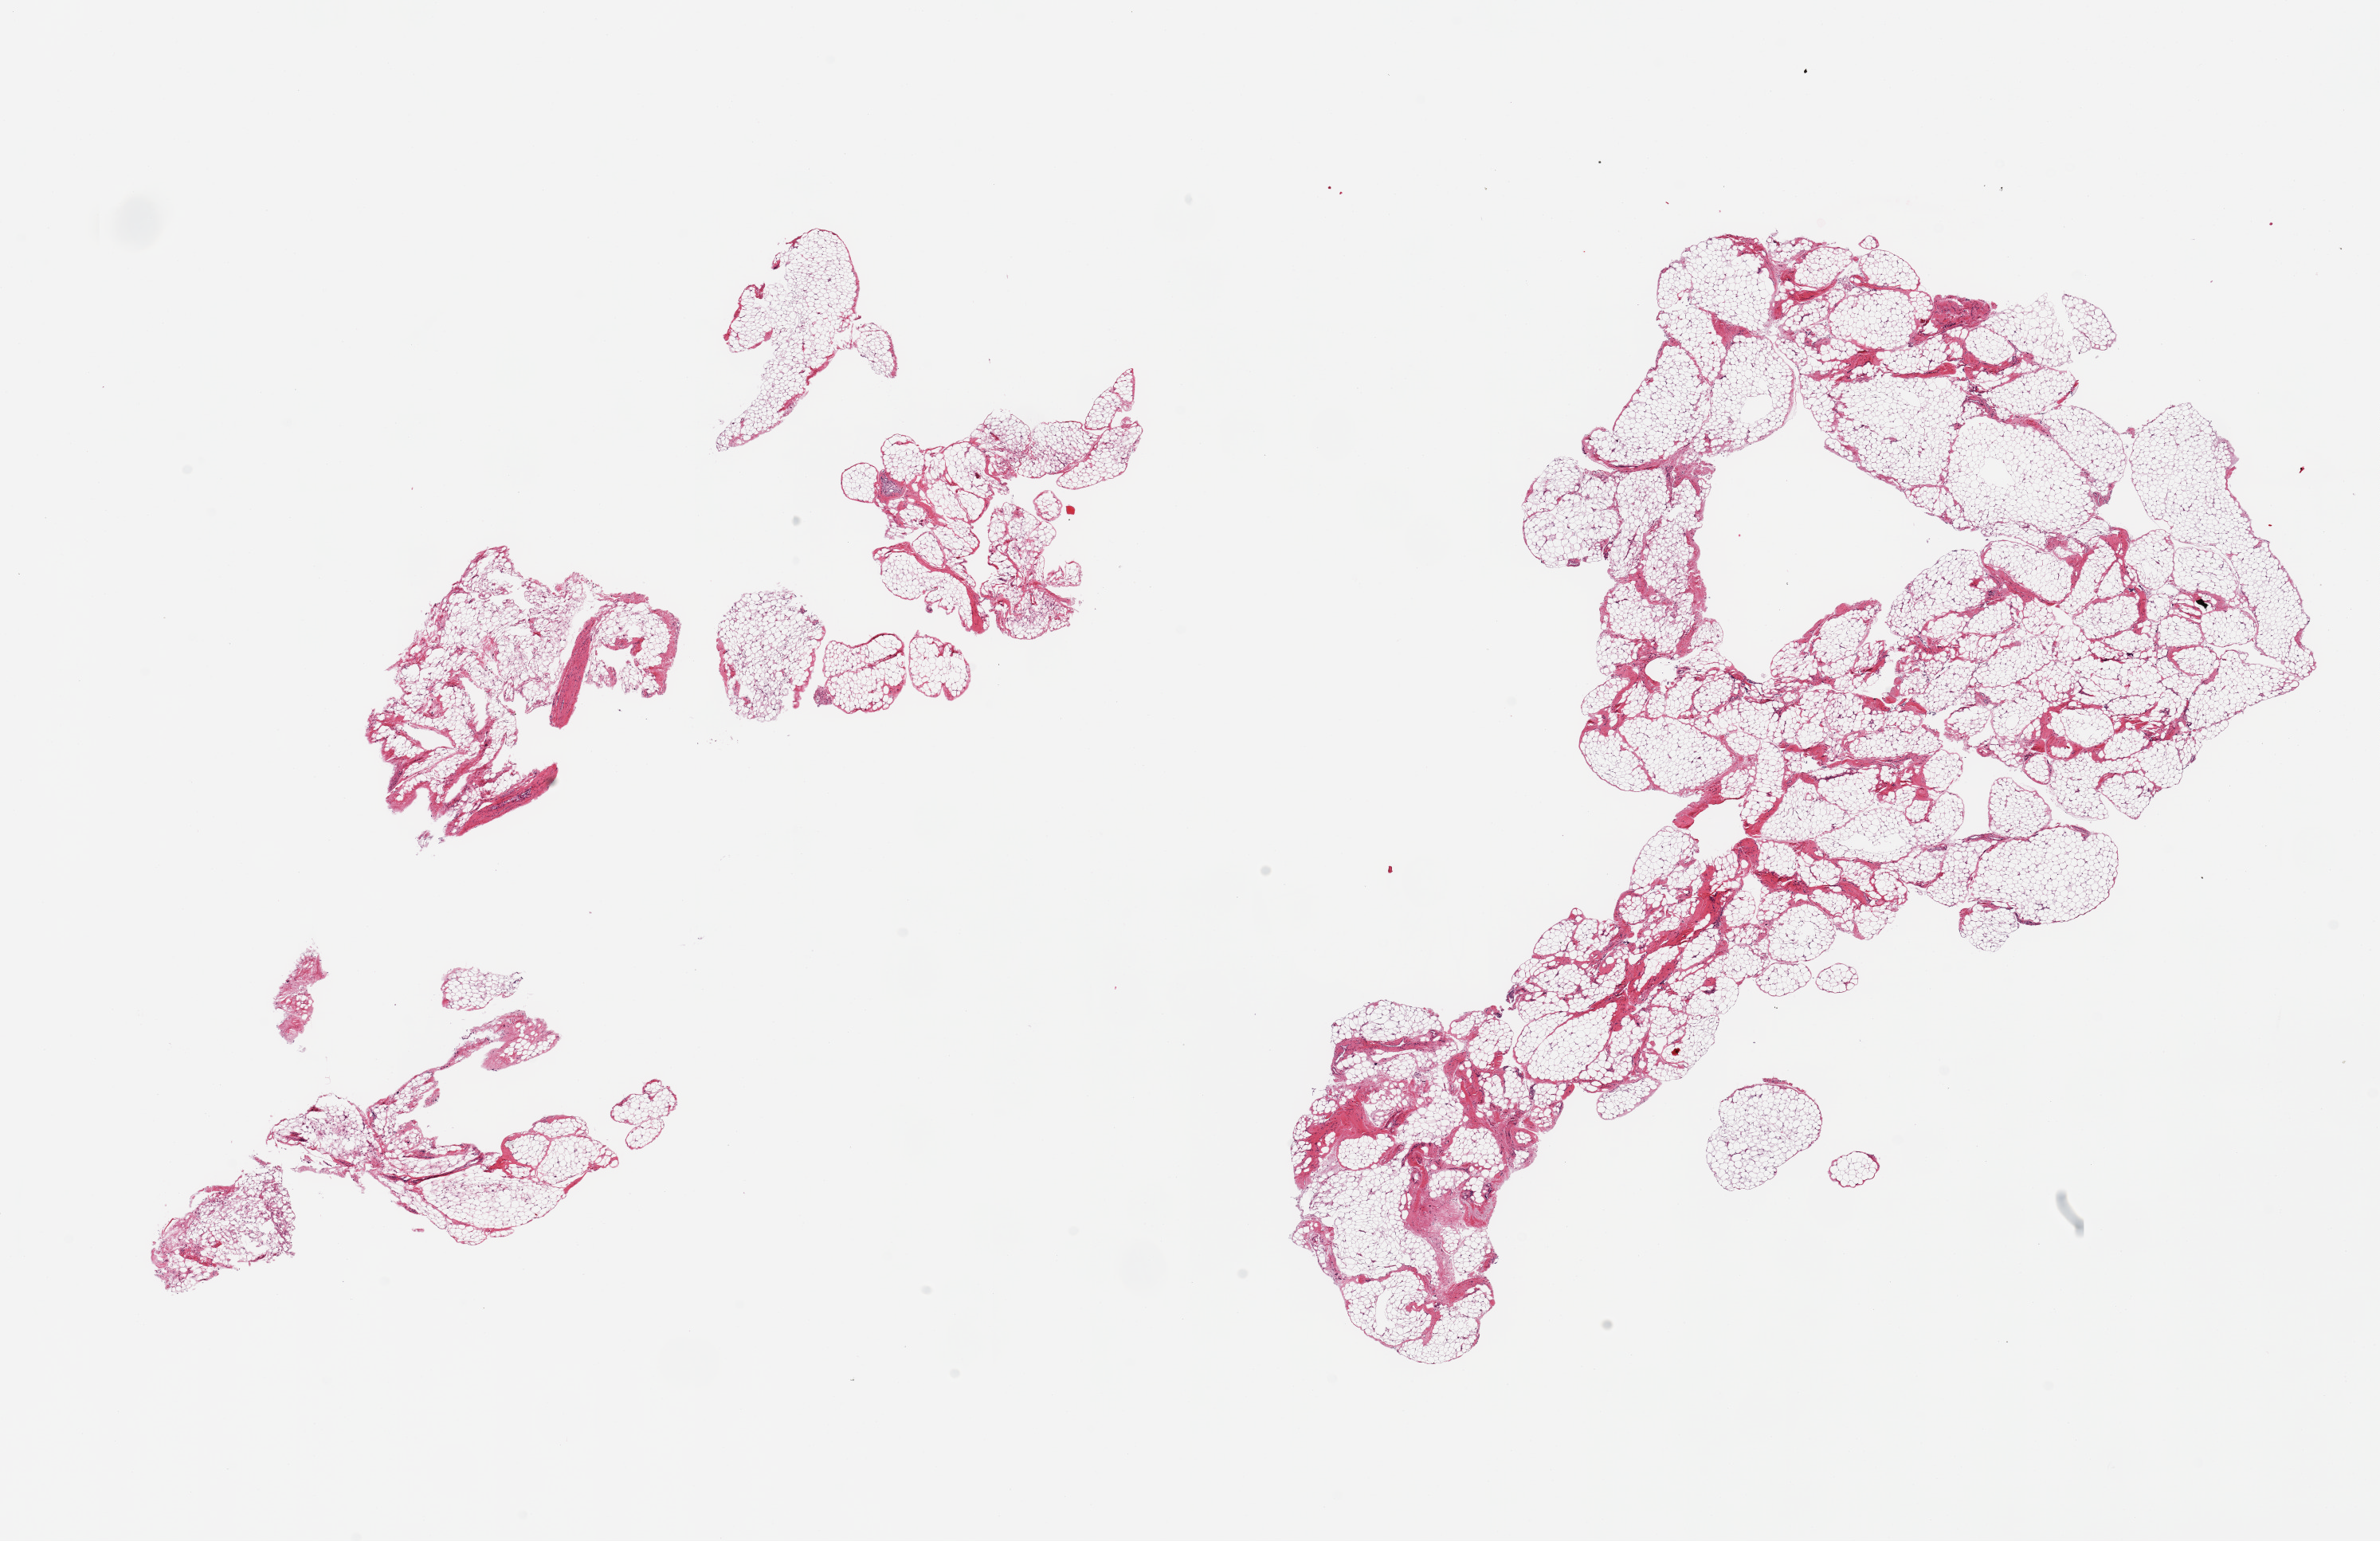
Digitized haematoxylin and eosin-stained section — whole scanned area (about 23.6 x 15.3 mm) shown as a low-resolution overview; PAXgene-fixed paraffin-embedded (PFPE) section; section of omentum (target tissue); donor tissue sample. Donor: male.
• review note (as recorded): 2 pieces; adipose tissue with 10% fibrous content